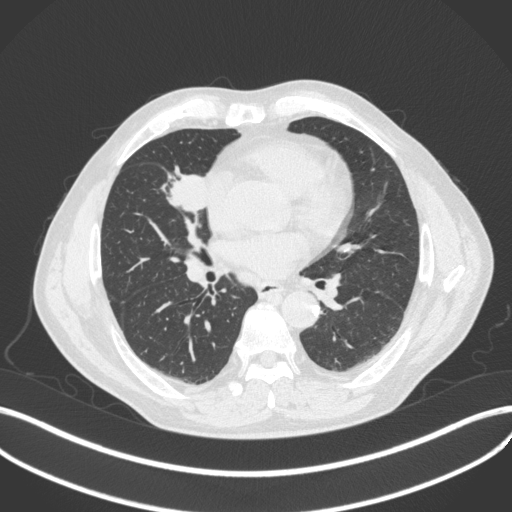
Chest CT, one axial slice; slice 194 of 429 in the series (ordered by position); lung window (W 1500 / L -600 HU); 1 mm slice thickness; 512 × 512 image matrix, field of view 400 × 400 mm. Male patient, age 61 years. From the clinical record (not read from this slice): clinical TNM (as recorded): T2b N1 M0.
Annotated regions visible in this slice (bounding box drawn by a radiologist):
- lung tumour (recorded histology: squamous cell carcinoma): bounding box [x1, y1, x2, y2] px = [163, 163, 208, 212]